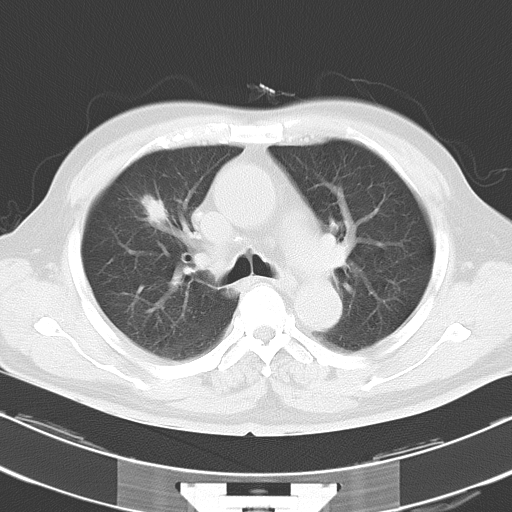
Chest CT, one axial slice; position 19 of 29 along the scan axis; reconstruction kernel B70f; lung window (W 1500 / L -600 HU); 512 × 512 image matrix. Male patient, age 70 years. Case-level facts recorded for this patient, not image findings: clinical TNM (as recorded): T1b N0 M0; histopathological grade: G2.
Outlined on this slice (bounding box drawn by a radiologist):
- lung tumour (recorded histology: adenocarcinoma): bounding box (x1, y1, x2, y2) in pixels: (135, 189, 172, 229)